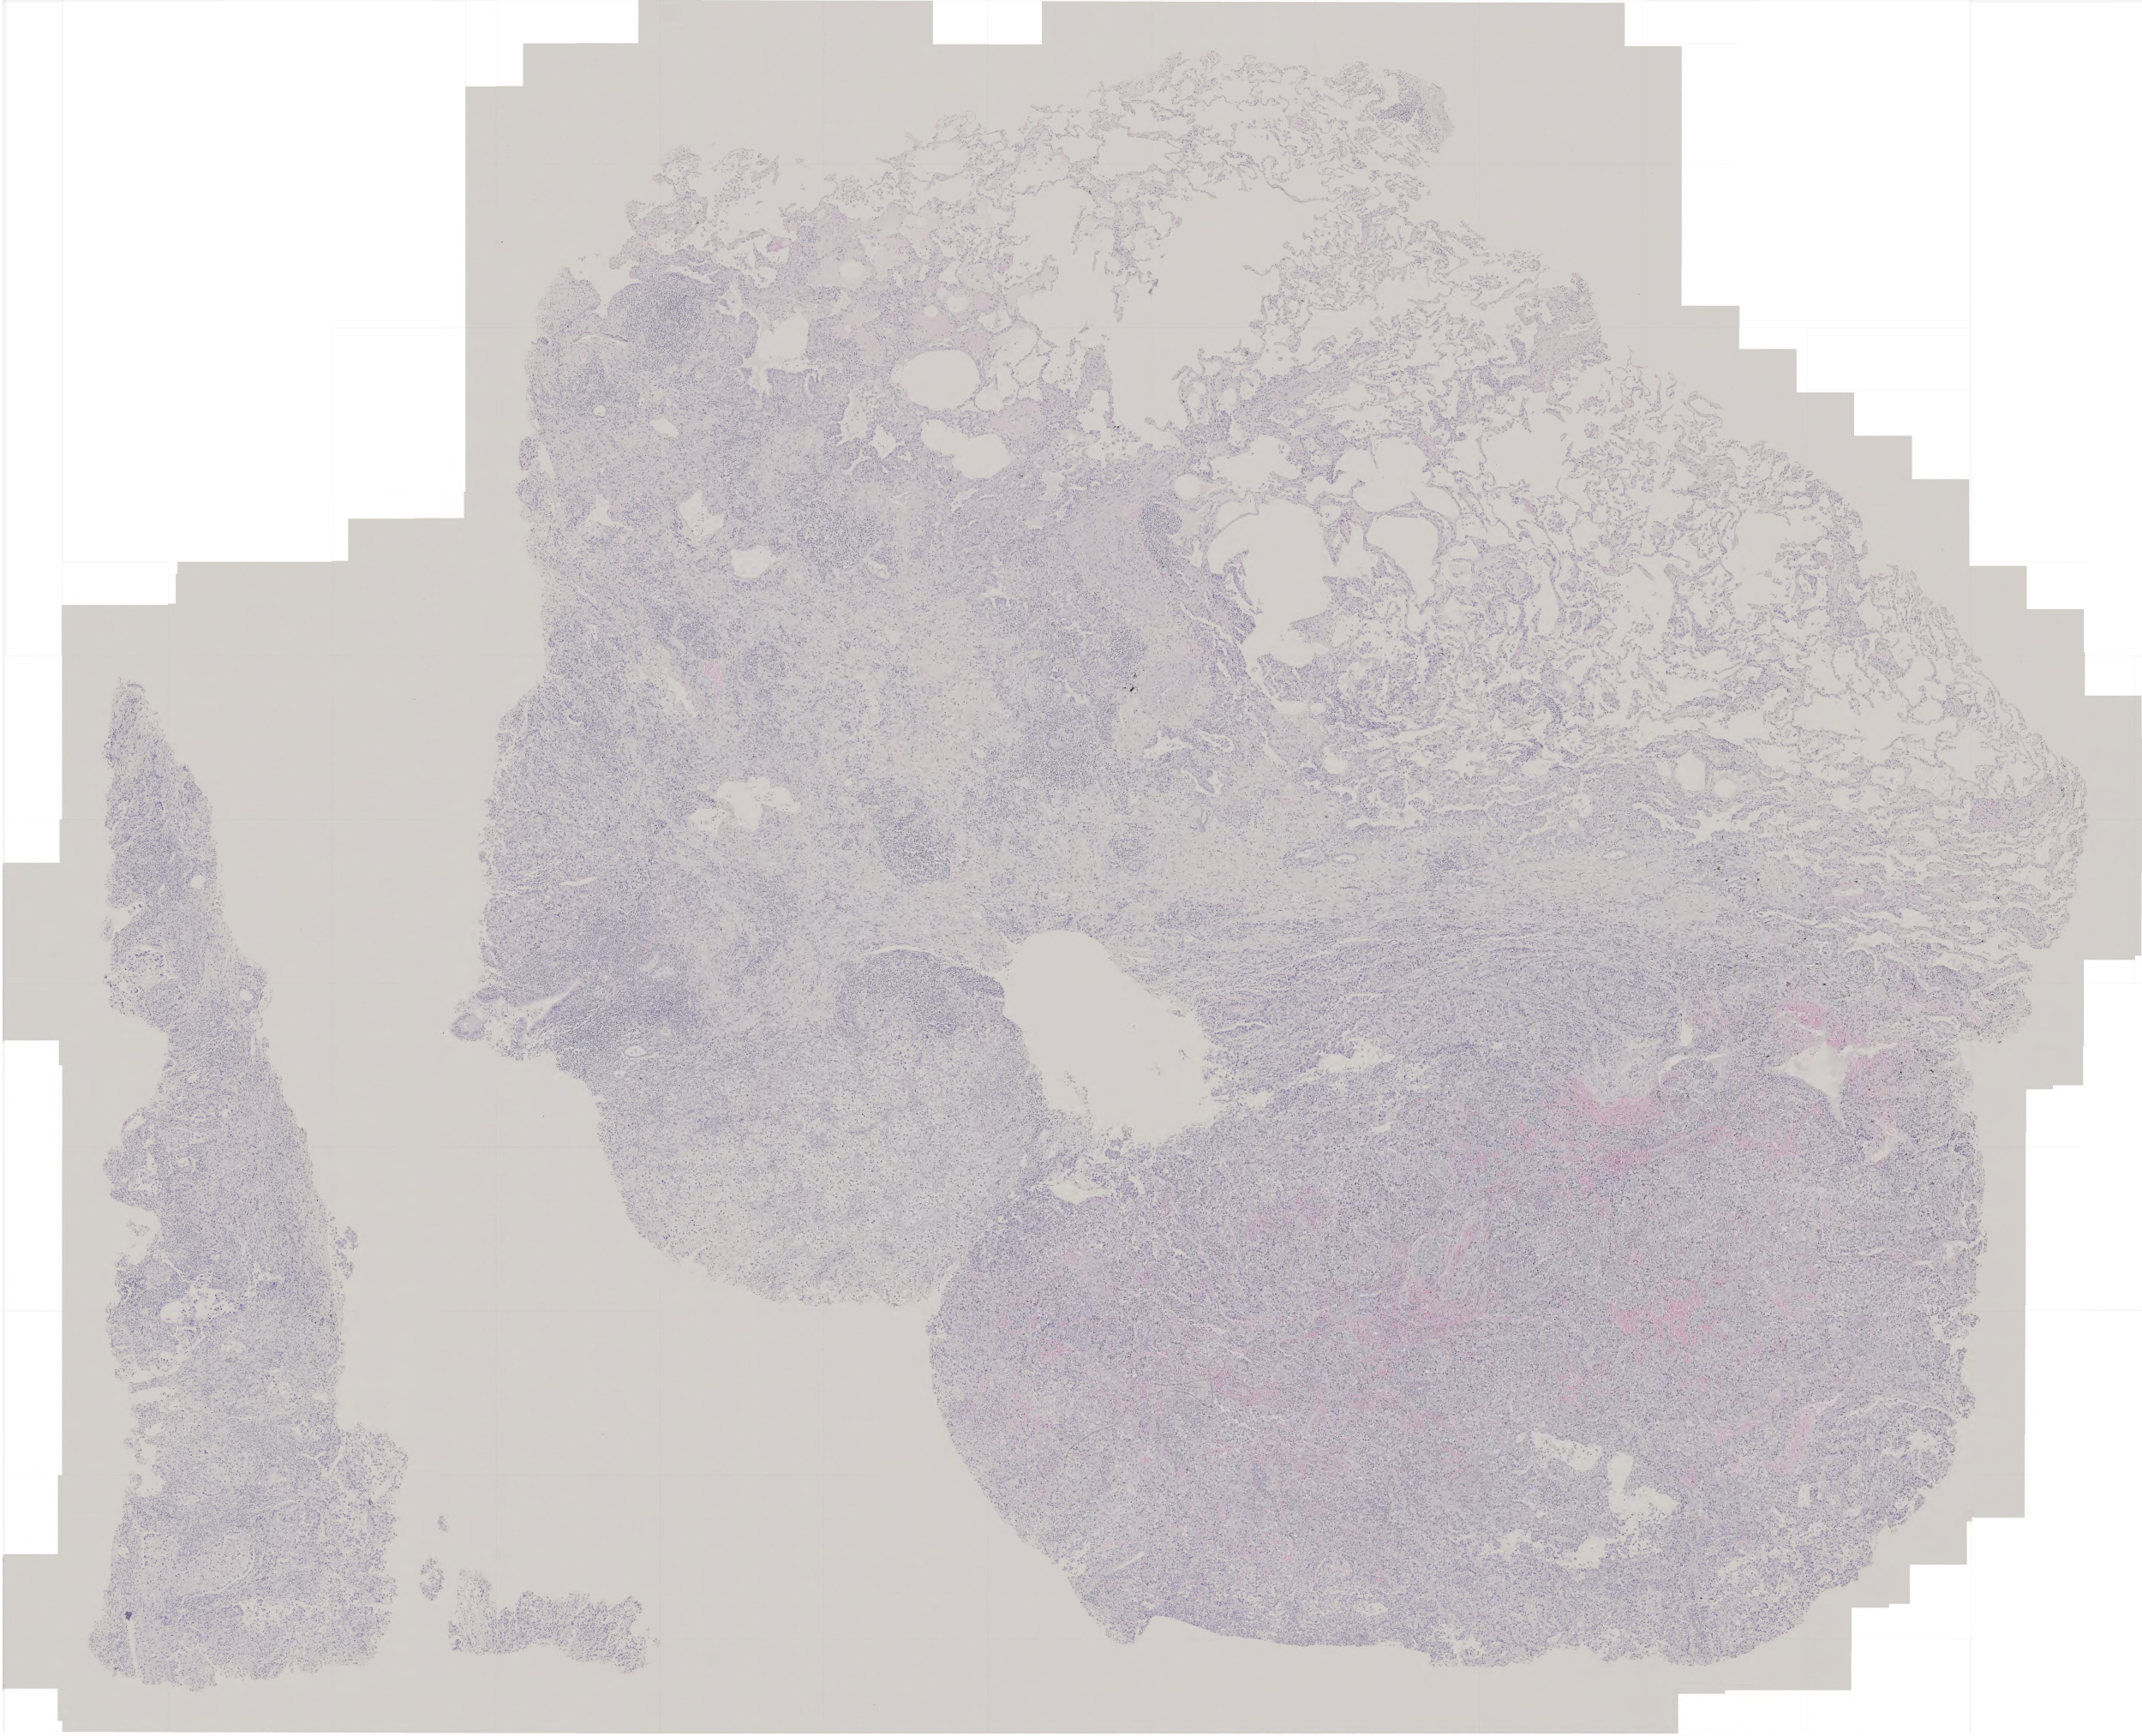
Digitized H&E-stained tissue section (whole slide), whole scanned area (about 5.0 x 4.1 mm) shown as a low-resolution overview; formalin-fixed paraffin-embedded (FFPE) diagnostic section; lung, primary tumour sample. Male patient; age at initial diagnosis 67 years.
Pathologic diagnosis: Adenocarcinoma, NOS. AJCC pathologic stage: IIIA (6th edition).